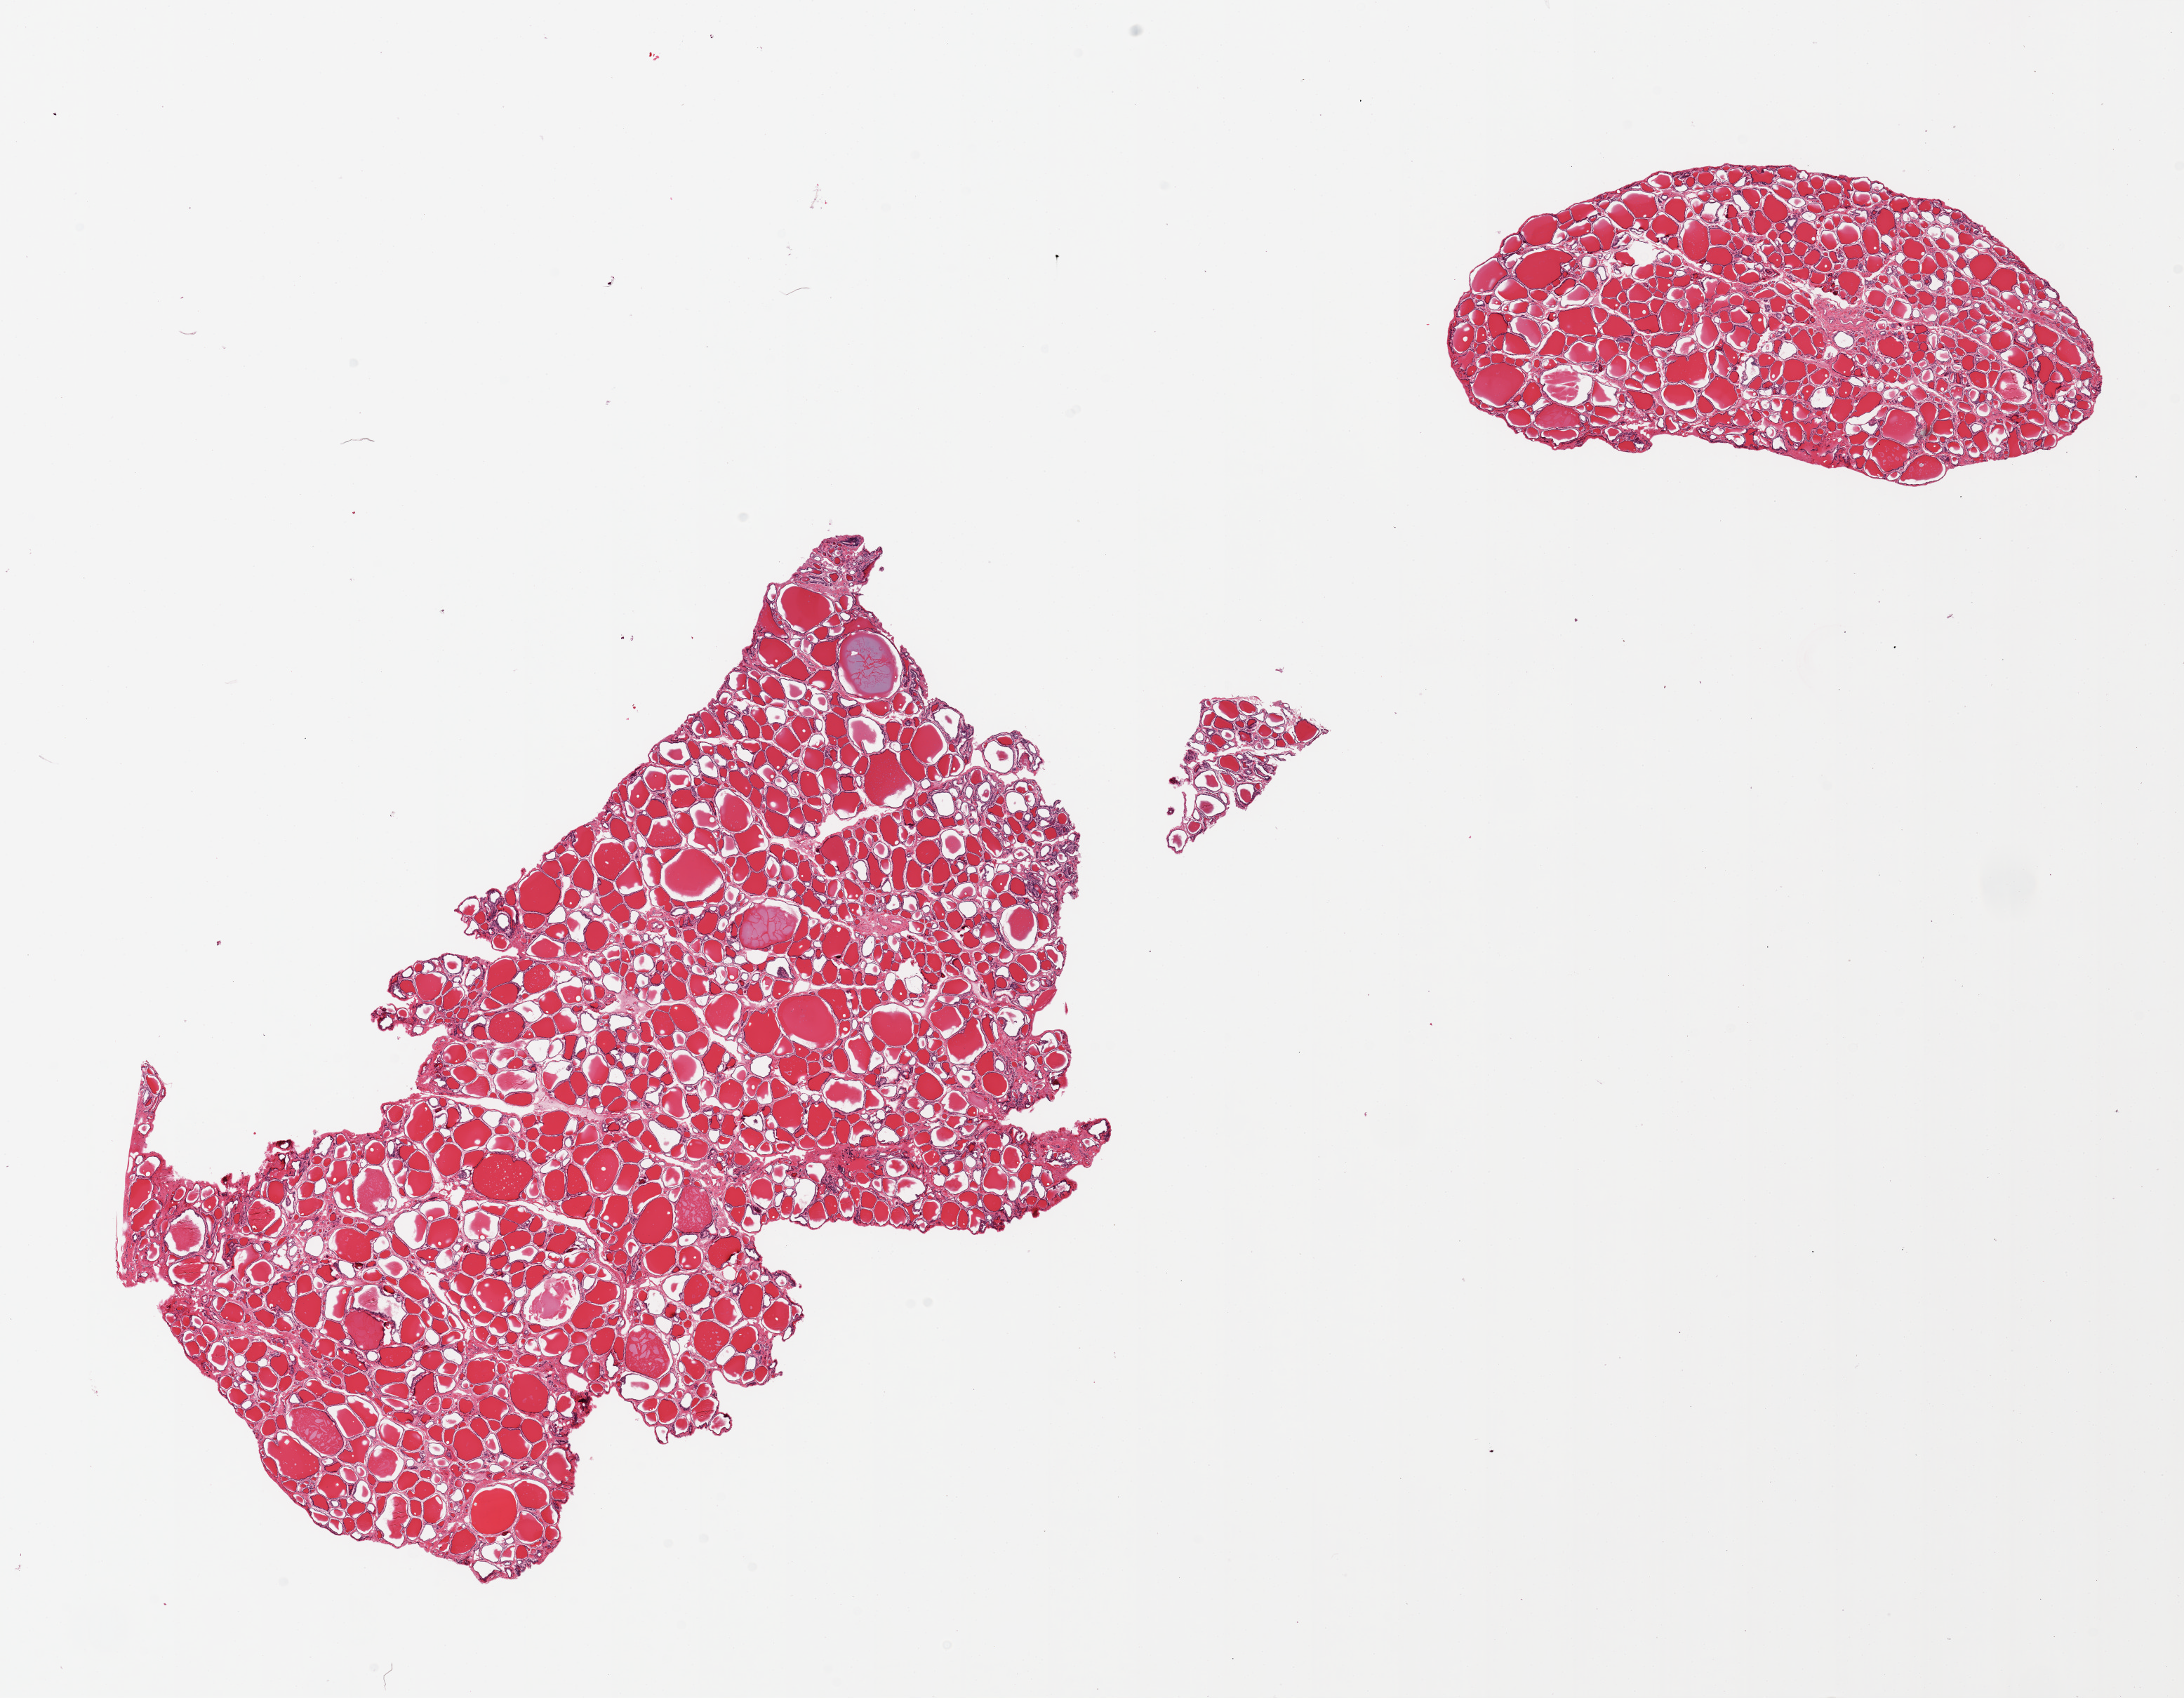
Whole-slide image, haematoxylin and eosin stain, brightfield — whole scanned area (about 24.6 x 19.1 mm) shown as a low-resolution overview; PAXgene-fixed paraffin-embedded (PFPE) section; sampled site (target tissue): thyroid; donor tissue sample. Donor sex: male.
Review note (as recorded): 2 pieces.